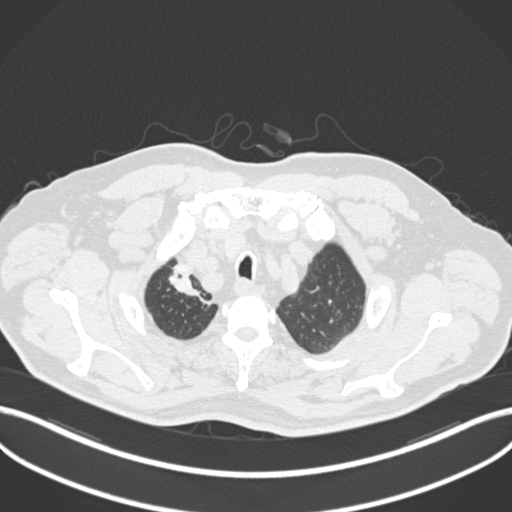
Chest CT, one axial slice; position 181 of 255 along the scan axis; 120 kVp; lung window (W 1500 / L -600 HU); 1 mm slice thickness; 512 × 512 image matrix, field of view 400 × 400 mm. Male patient, age 60 years. From the clinical record (not read from this slice): clinical TNM (as recorded): T1b N1 M0.
Structures marked on this image (bounding box drawn by a radiologist):
- lung tumour (recorded histology: squamous cell carcinoma): bounding box <161,268,205,307> (left, top, right, bottom; pixels)